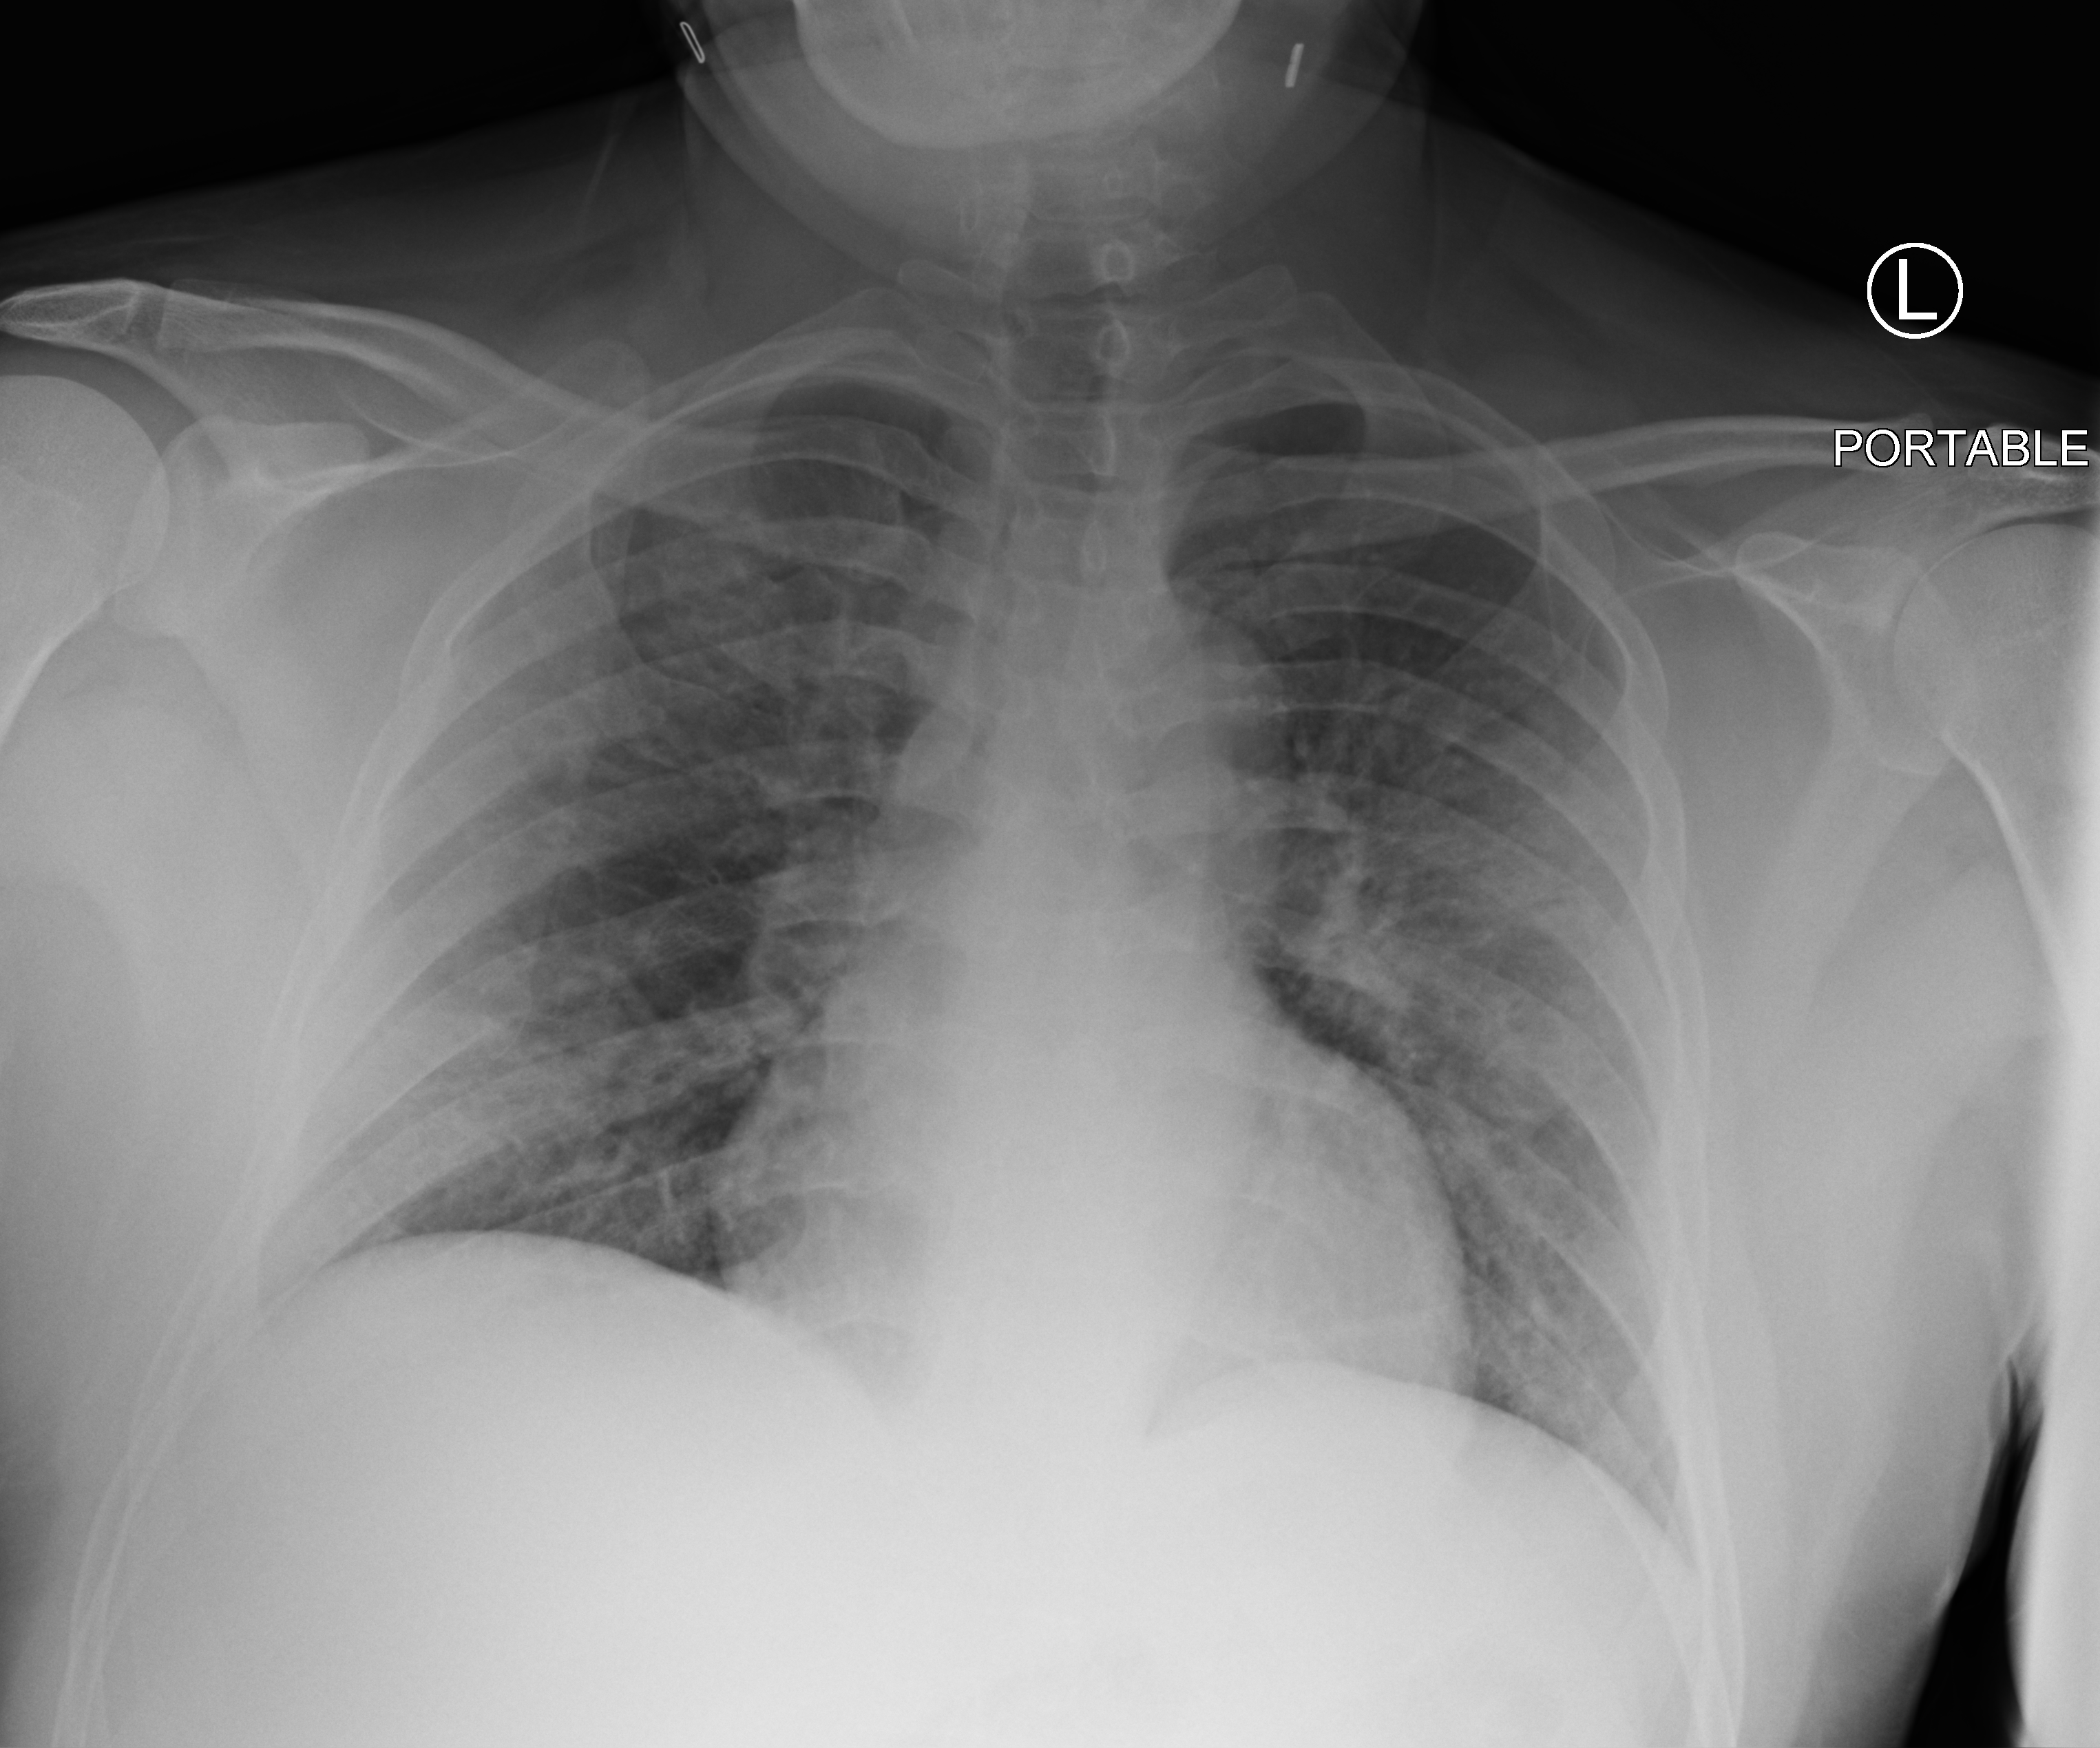
Portable chest radiograph; anteroposterior (AP) projection. Male patient hospitalised with COVID-19, age 18–59 years.
Hospital-stay facts (about this admission, not read from this image; timing relative to this image not recorded): length of hospital stay: 1 day; mechanically ventilated during this hospital stay: no.